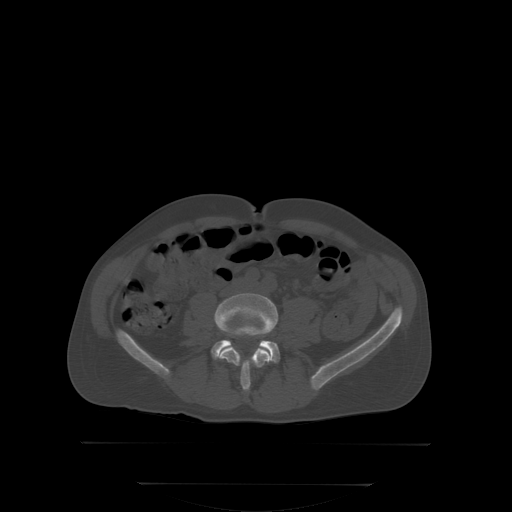
CT including the spine, one axial slice. Slice 103 of 350 in the series (ordered by position). Bone window (W 1800 / L 400 HU). 2.5 mm slice thickness. 512 × 512 image matrix, field of view 500 × 500 mm. Patient: male, 58 years. Case-level facts recorded for this patient, not image findings: primary cancer: prostate; vertebrae with lytic lesions (as recorded): L1.
Structures marked on this image (semi-automatically segmented with operator editing):
- L4 vertebra: bounding box [x1, y1, x2, y2] px = [216, 293, 278, 391]
- L5 vertebra: [212, 340, 280, 361]